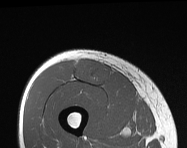
MRI of an extremity soft-tissue mass, one axial slice; position 52 of 114 along the scan axis; MR volume resampled by the dataset authors to the PET/CT grid (not the native acquisition matrix); 3.27 mm slice thickness; 187 × 148 image matrix, field of view 183 × 145 mm. Male patient. Case-level facts recorded for this patient, not image findings: histological type: pleiomorphic leiomyosarcoma; grade: intermediate; site of the primary tumour: right thigh.
Structures marked on this image (expert contour drawn on MRI and transferred to this co-registered scan by the dataset authors):
- gross tumour volume including surrounding oedema: bounding box <73,59,112,85> (left, top, right, bottom; pixels)